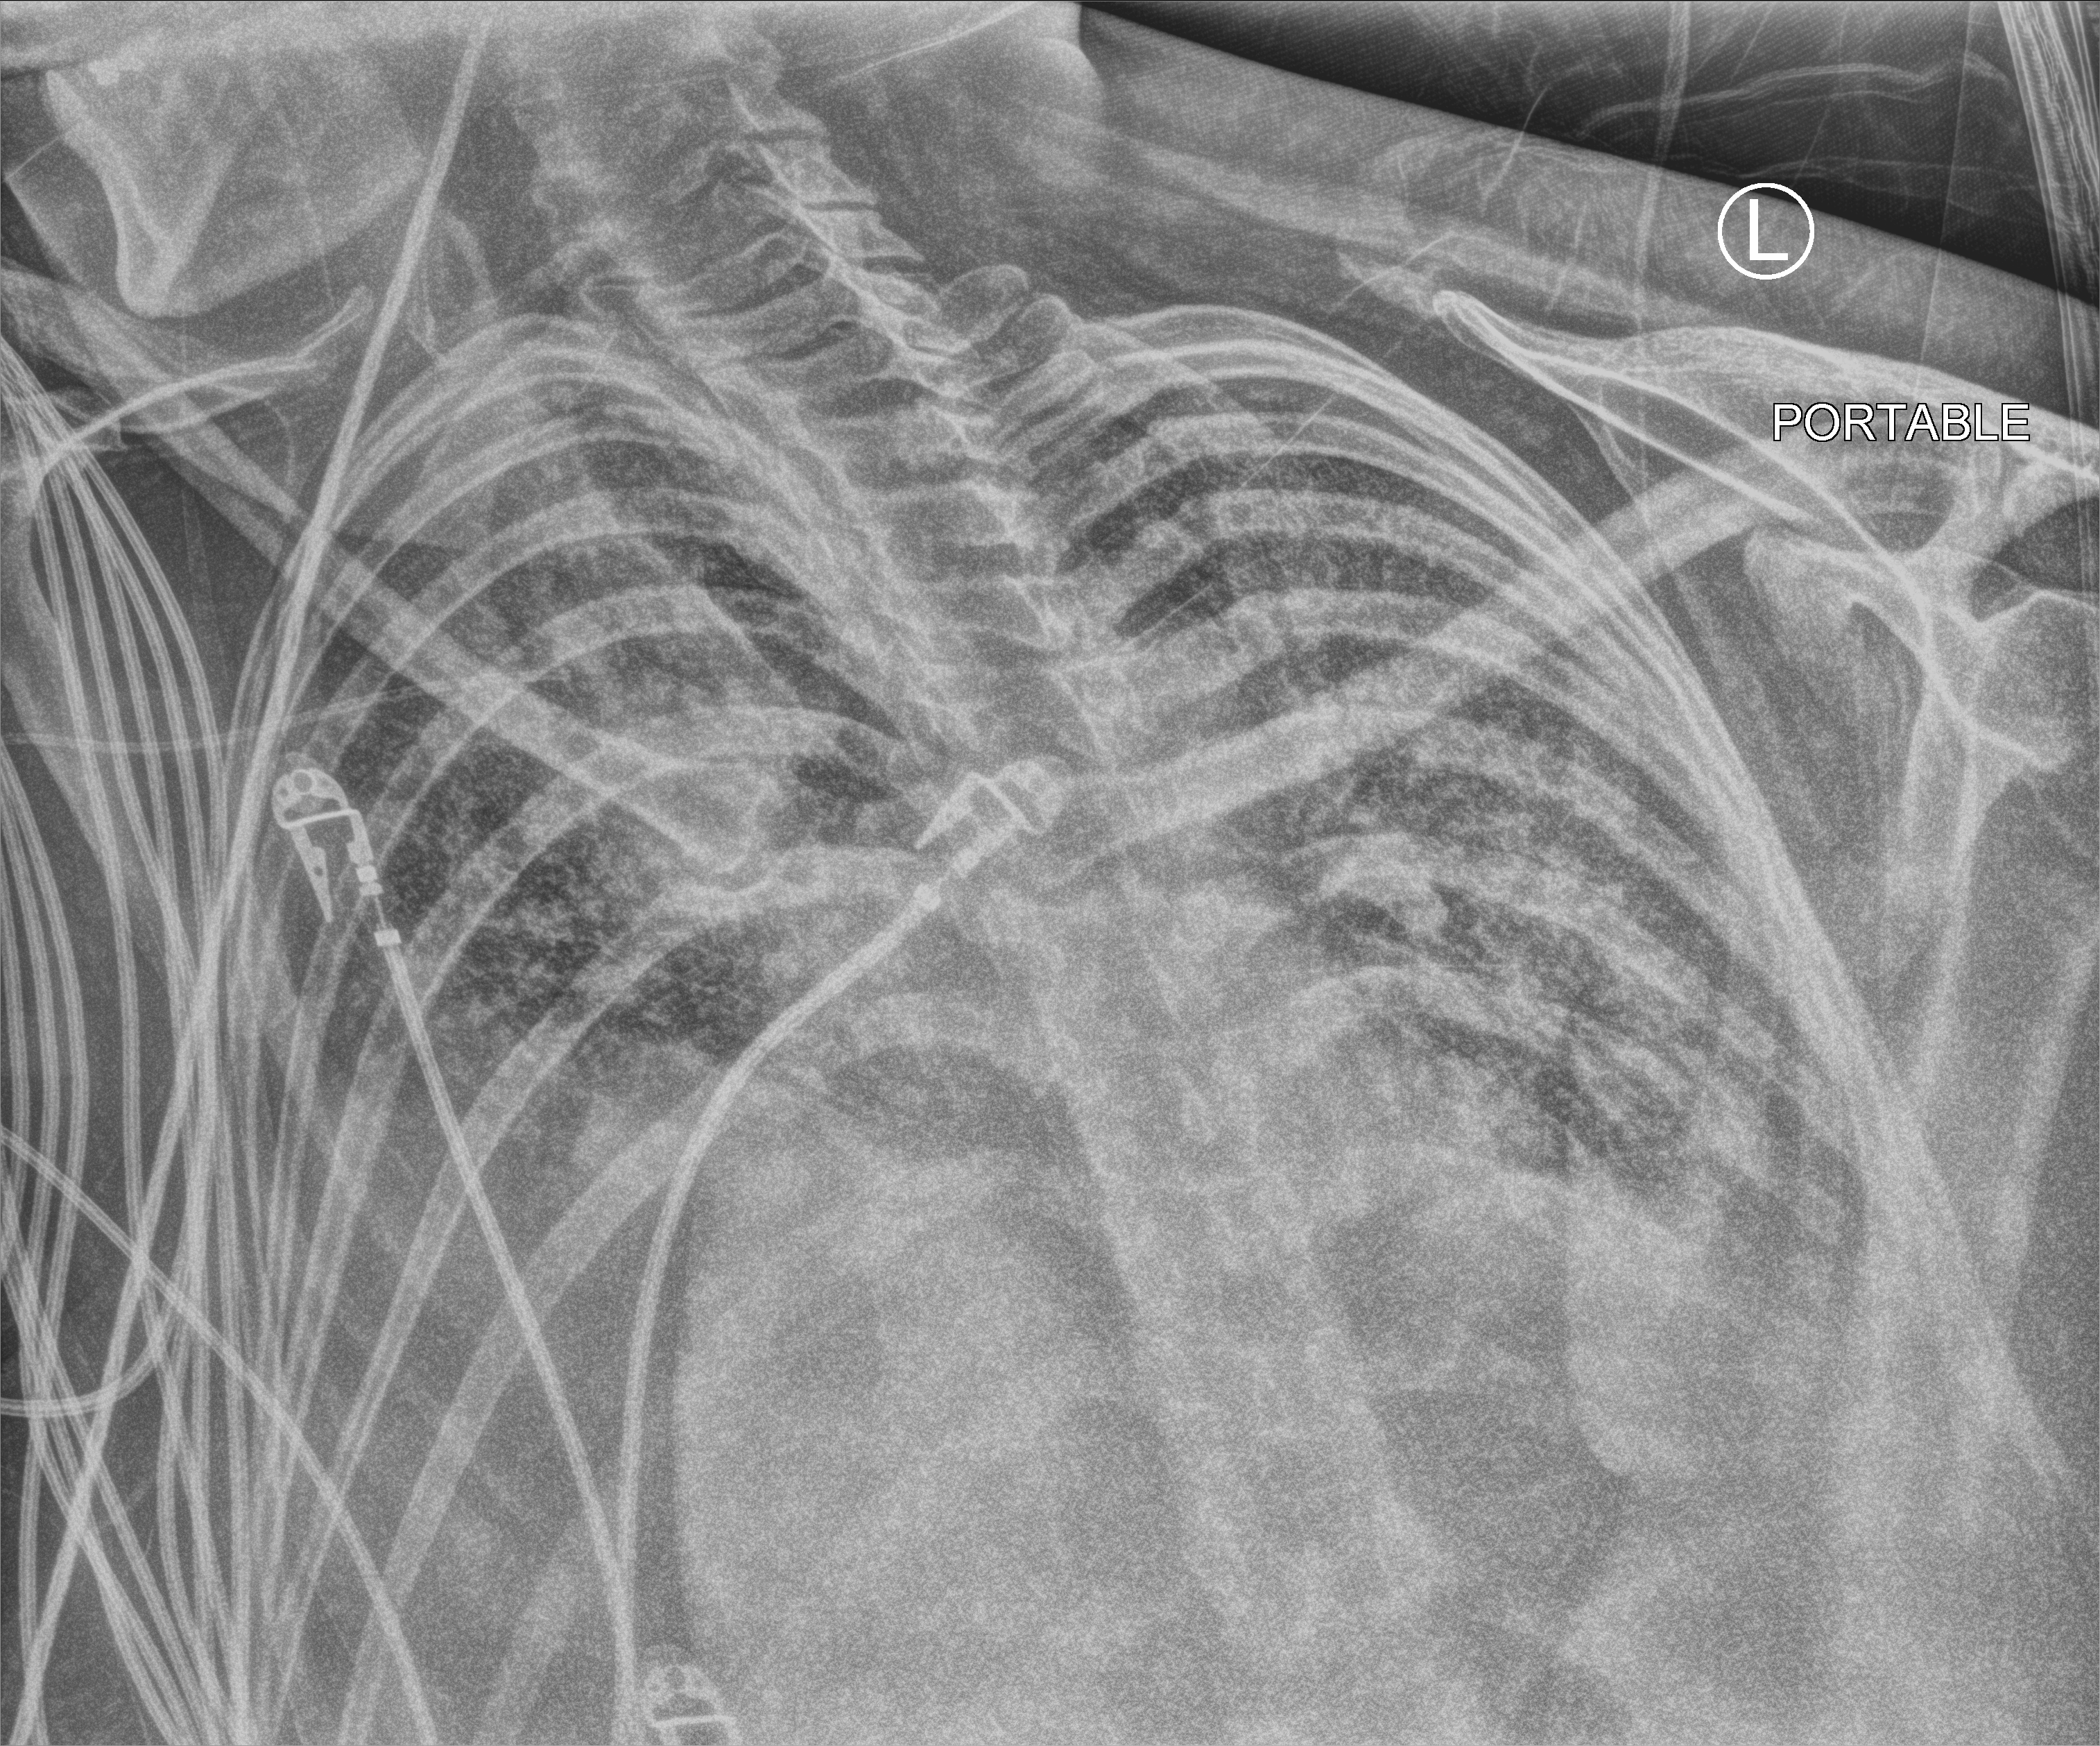
Bedside chest radiograph (computed radiography). Female patient hospitalised with COVID-19, age 18–59 years.
Admission-level facts for this patient (not findings on this image; timing relative to this image not recorded): hypertension (admission record): no.